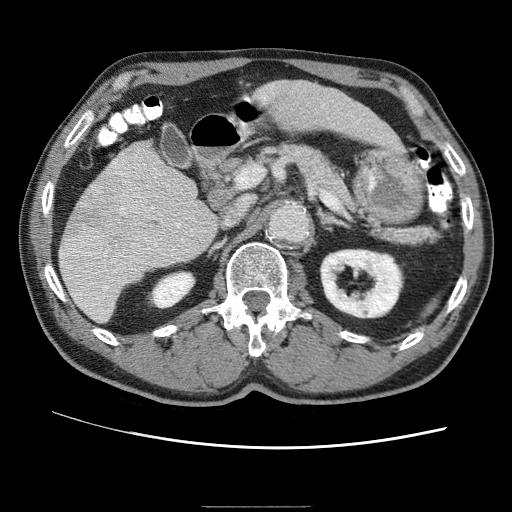
Contrast-enhanced abdominal CT (liver protocol), one axial slice; slice 23 of 75 in the series (ordered by position); one of 2 acquisitions stored at this slice position; soft-tissue window (W 400 / L 40 HU); 512 × 512 image matrix. Case-level facts recorded for this patient, not image findings: diagnosis: hepatocellular carcinoma (patient treated with transarterial chemoembolisation; whether this scan precedes or follows treatment is not stated here); TNM stage (as recorded): Stage-II.
Outlined on this slice (semi-automatic segmentation, software-assisted and operator-edited):
- liver parenchyma outside the tumour (the mass and vessels are separate outlines, so this box may not span the whole liver): bounding box [x1, y1, x2, y2] px = [60, 82, 365, 321]
- liver vessels: [70, 163, 193, 256]